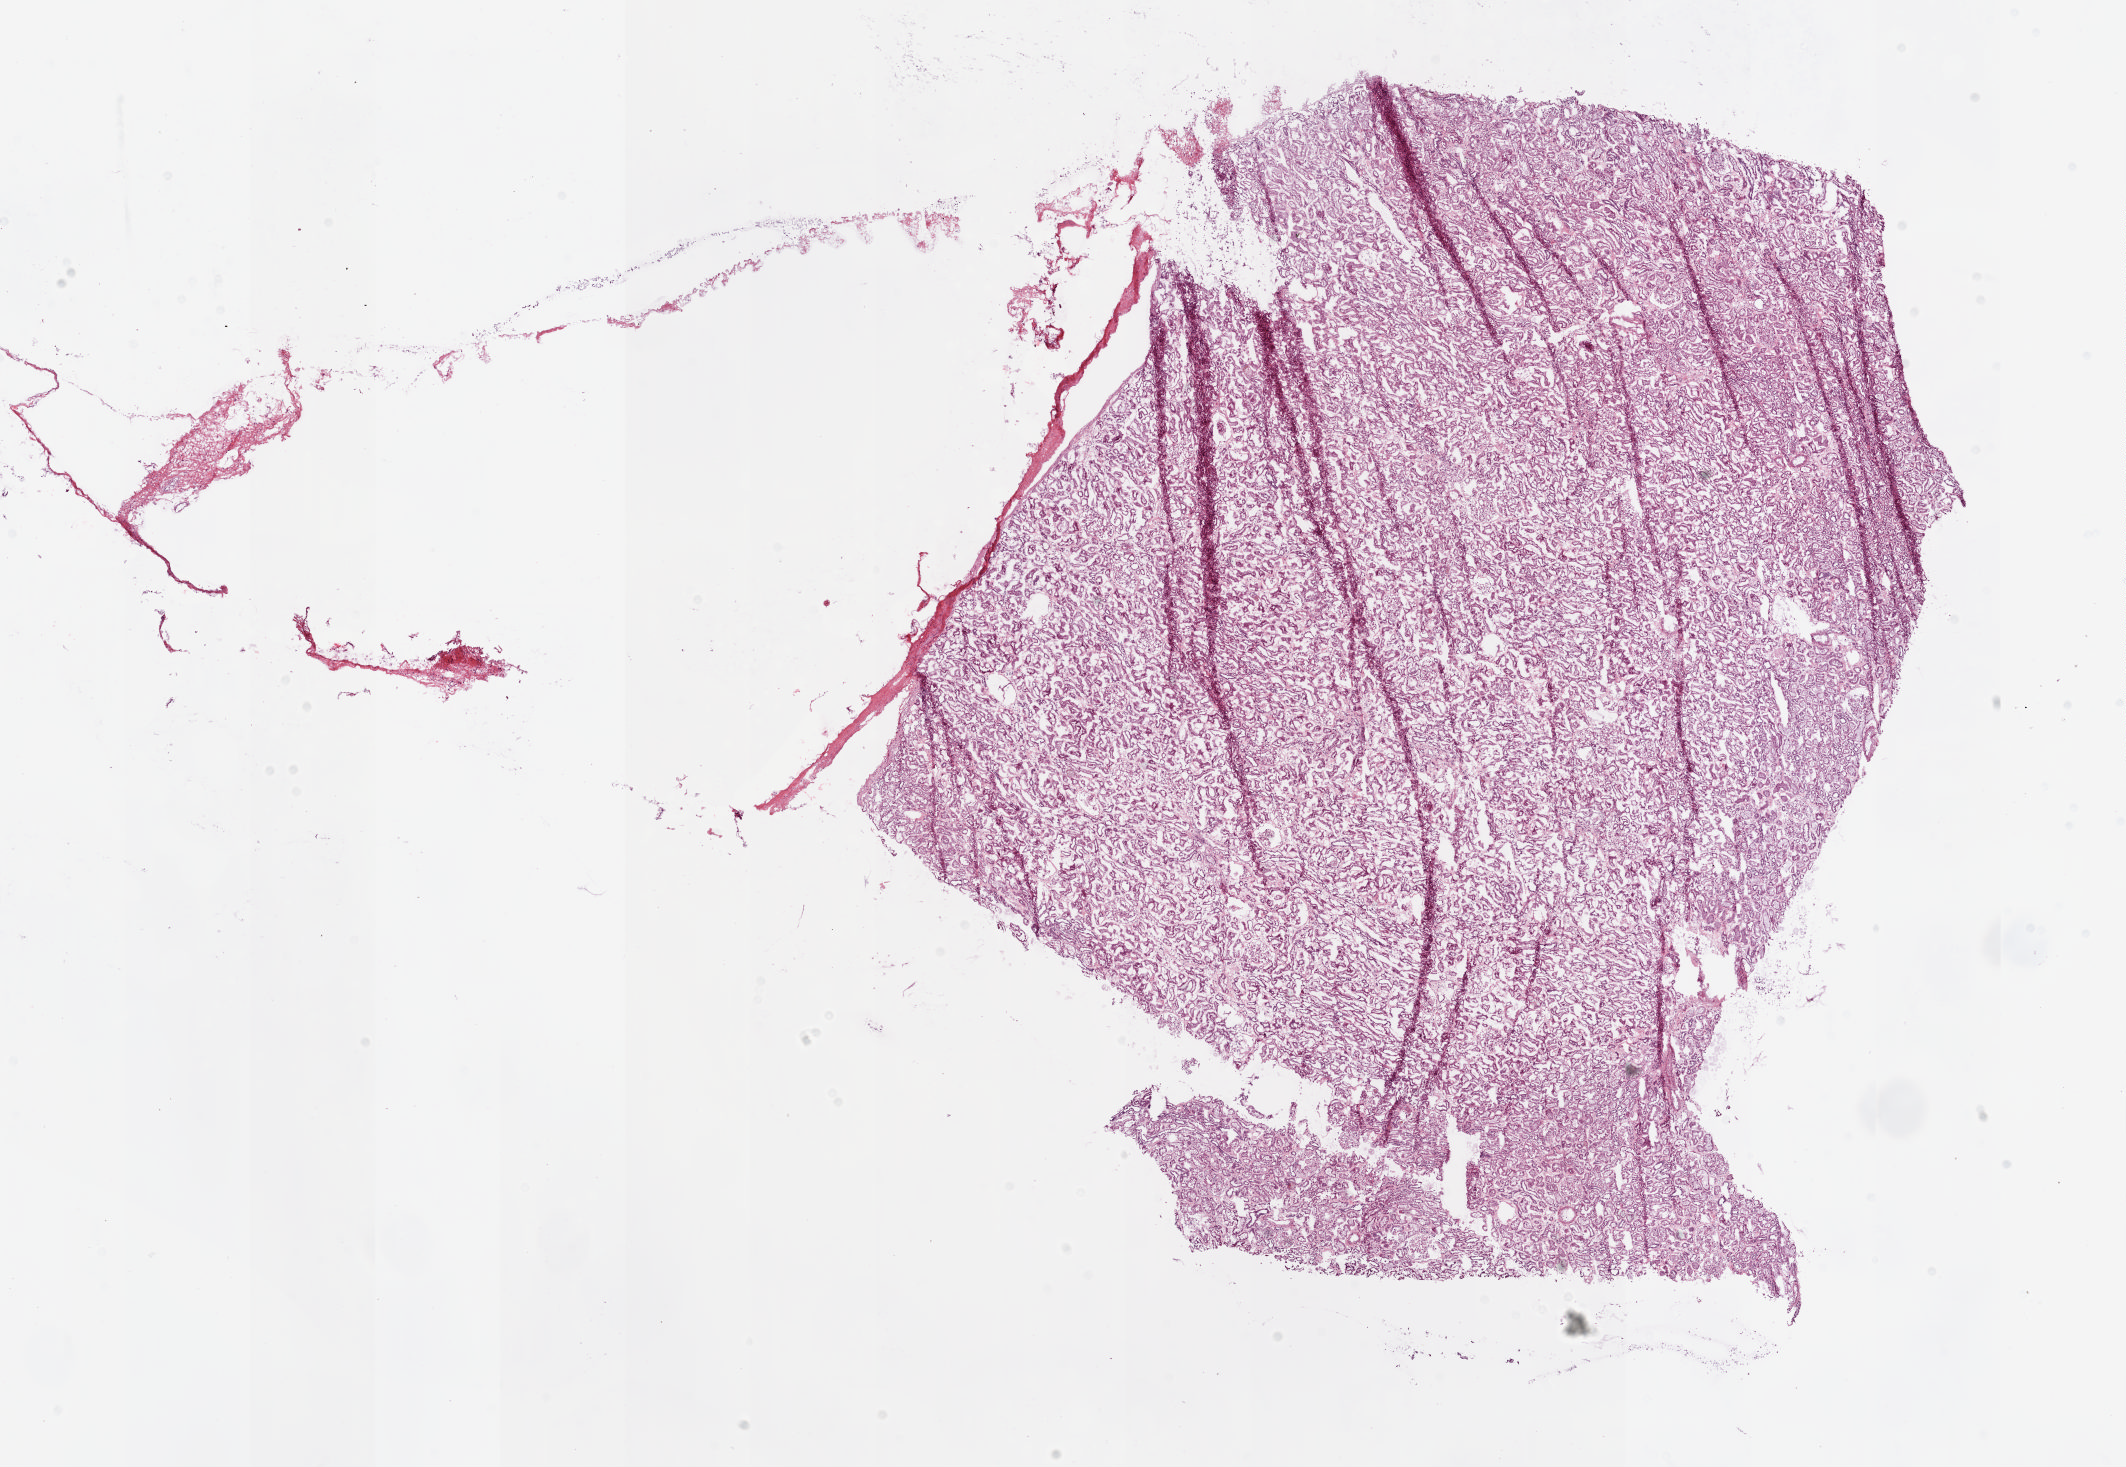
Digitized Hematoxylin and eosin (H&E) stained tissue section (whole slide) — a low-resolution overview of the entire scanned area, about 16.9 x 11.6 mm (from a 20x scan), frozen section, solid tissue normal (non-tumour tissue) sample from the kidney. Patient: male, age at initial diagnosis 55 years.
This section: solid tissue normal (non-tumour) sample from the same patient. Patient diagnosis: Clear cell adenocarcinoma, NOS.